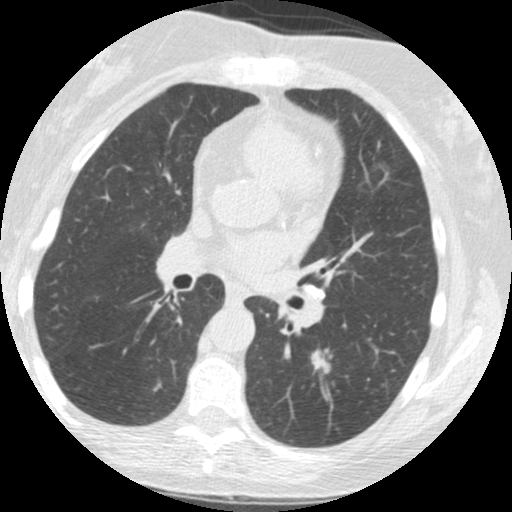
Chest CT (low-dose screening protocol), one axial image. Baseline annual screen. Lung window (W 1500 / L -600 HU). 512 × 512 image matrix. Female, age 61 years at enrolment.
- Lesion marked by an expert reader, bounding box (x1, y1, x2, y2) in pixels: (302, 338, 350, 392).
- Screening reader's record for this exam (one nodule recorded; not confirmed to be the boxed lesion): non-calcified nodule or mass ≥4 mm, left lower lobe, 12 × 11 mm, spiculated (stellate) margins, soft tissue attenuation.
- Official screen result: positive, change unspecified: nodule(s) >= 4 mm or enlarging nodule(s), mass(es), or other non-specific abnormalities suspicious for lung cancer.
- Lung cancer was diagnosed 440 days after this screen (after the second annual screen): squamous cell carcinoma, NOS, left lower lobe, moderately differentiated (G2), stage IA (AJCC 6th edition), 12 mm at pathology.